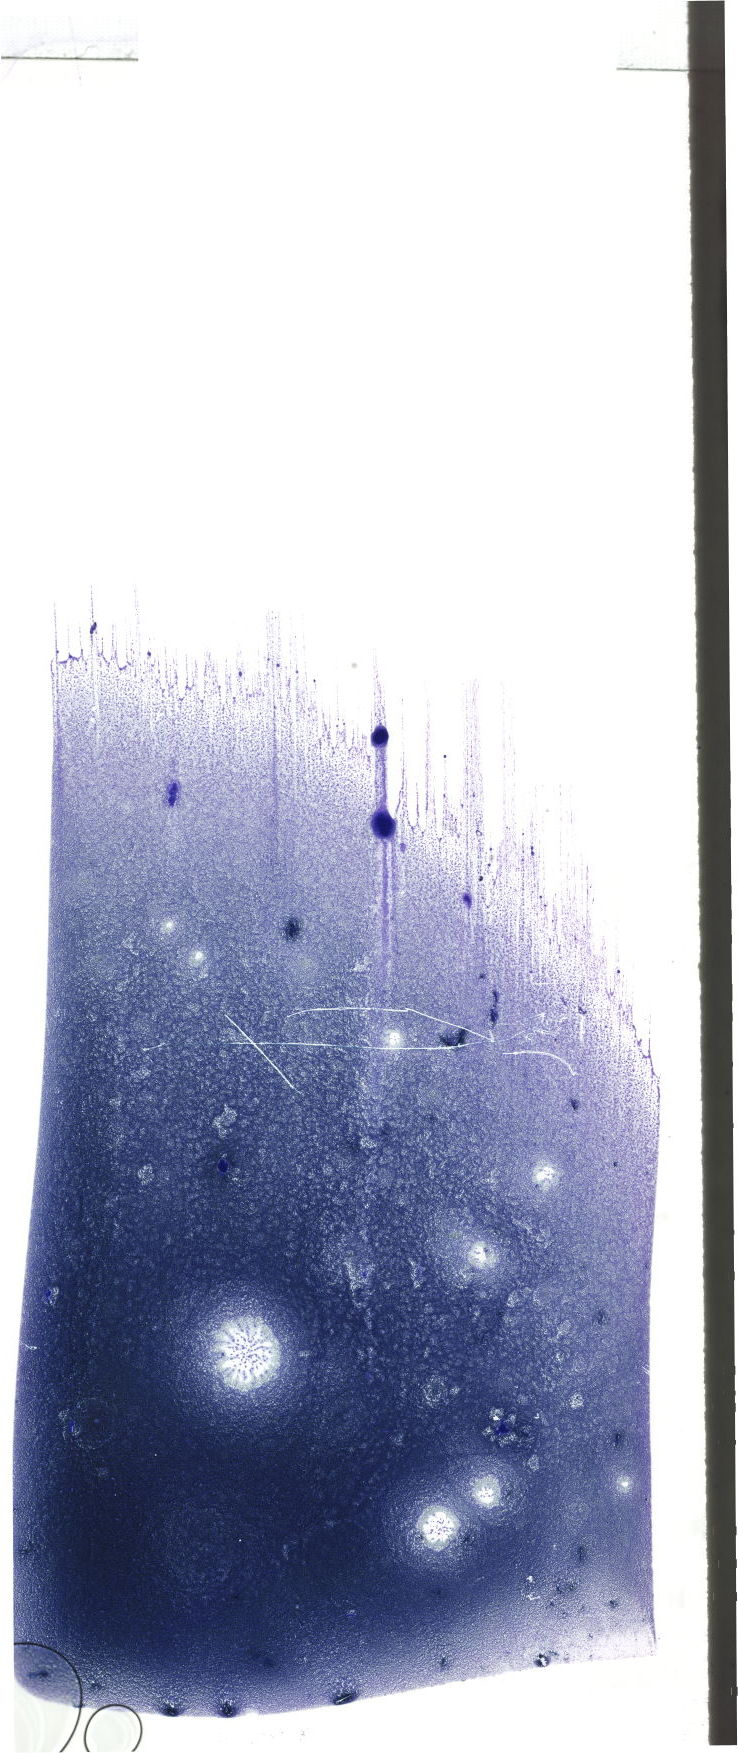
Whole-slide image of a May-Grünwald–Giemsa-stained bone marrow aspirate smear, low-resolution overview of the scanned area, about 20.9 x 49.7 mm. Patient sex: male.
Diagnosis: Chronic Phase Chronic Myeloid Leukemia, BCR-ABL1 Positive.